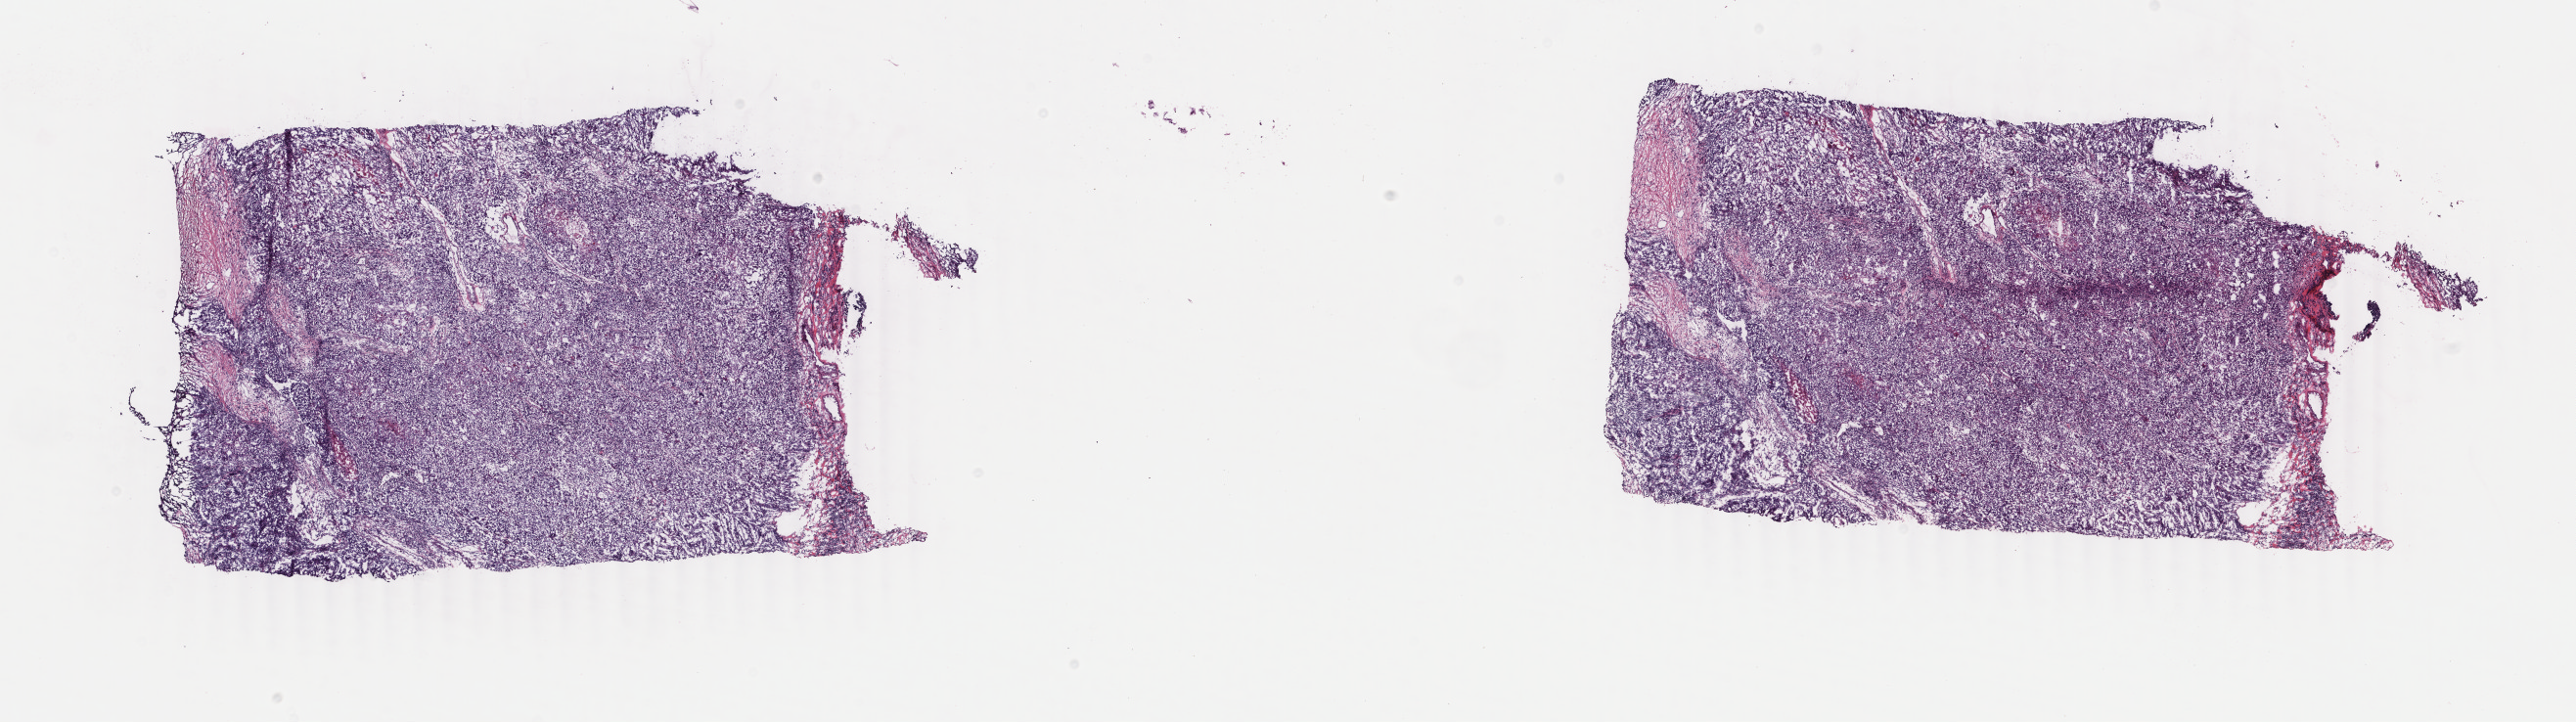
Whole-slide histology image, H&E, whole scanned area (about 20.9 x 5.9 mm) shown as a low-resolution overview; frozen section from the top of the tissue portion; sample: primary tumour, breast. Female patient; age at initial diagnosis 73 years.
Pathologic diagnosis: Infiltrating duct carcinoma, NOS.